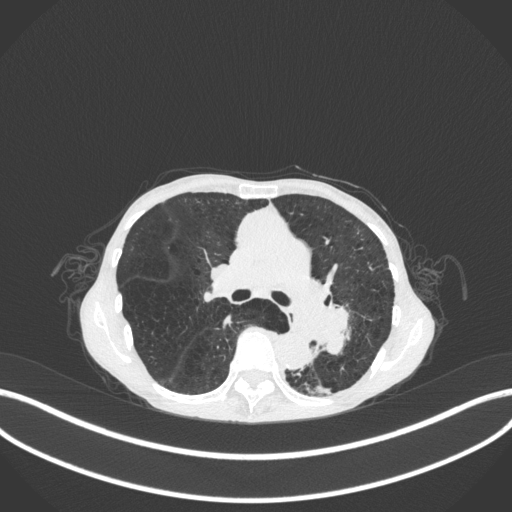
Chest CT, one axial slice. Slice 169 of 347 in the series (ordered by position). Lung window (W 1500 / L -600 HU). 512 × 512 image matrix, field of view 400 × 400 mm. Female patient, age 70 years. Case-level facts recorded for this patient, not image findings: clinical TNM (as recorded): T3 N0 M0.
Outlined on this slice (bounding box drawn by a radiologist):
- lung tumour (recorded histology: small cell carcinoma): bounding box [x1, y1, x2, y2] px = [306, 287, 360, 364]